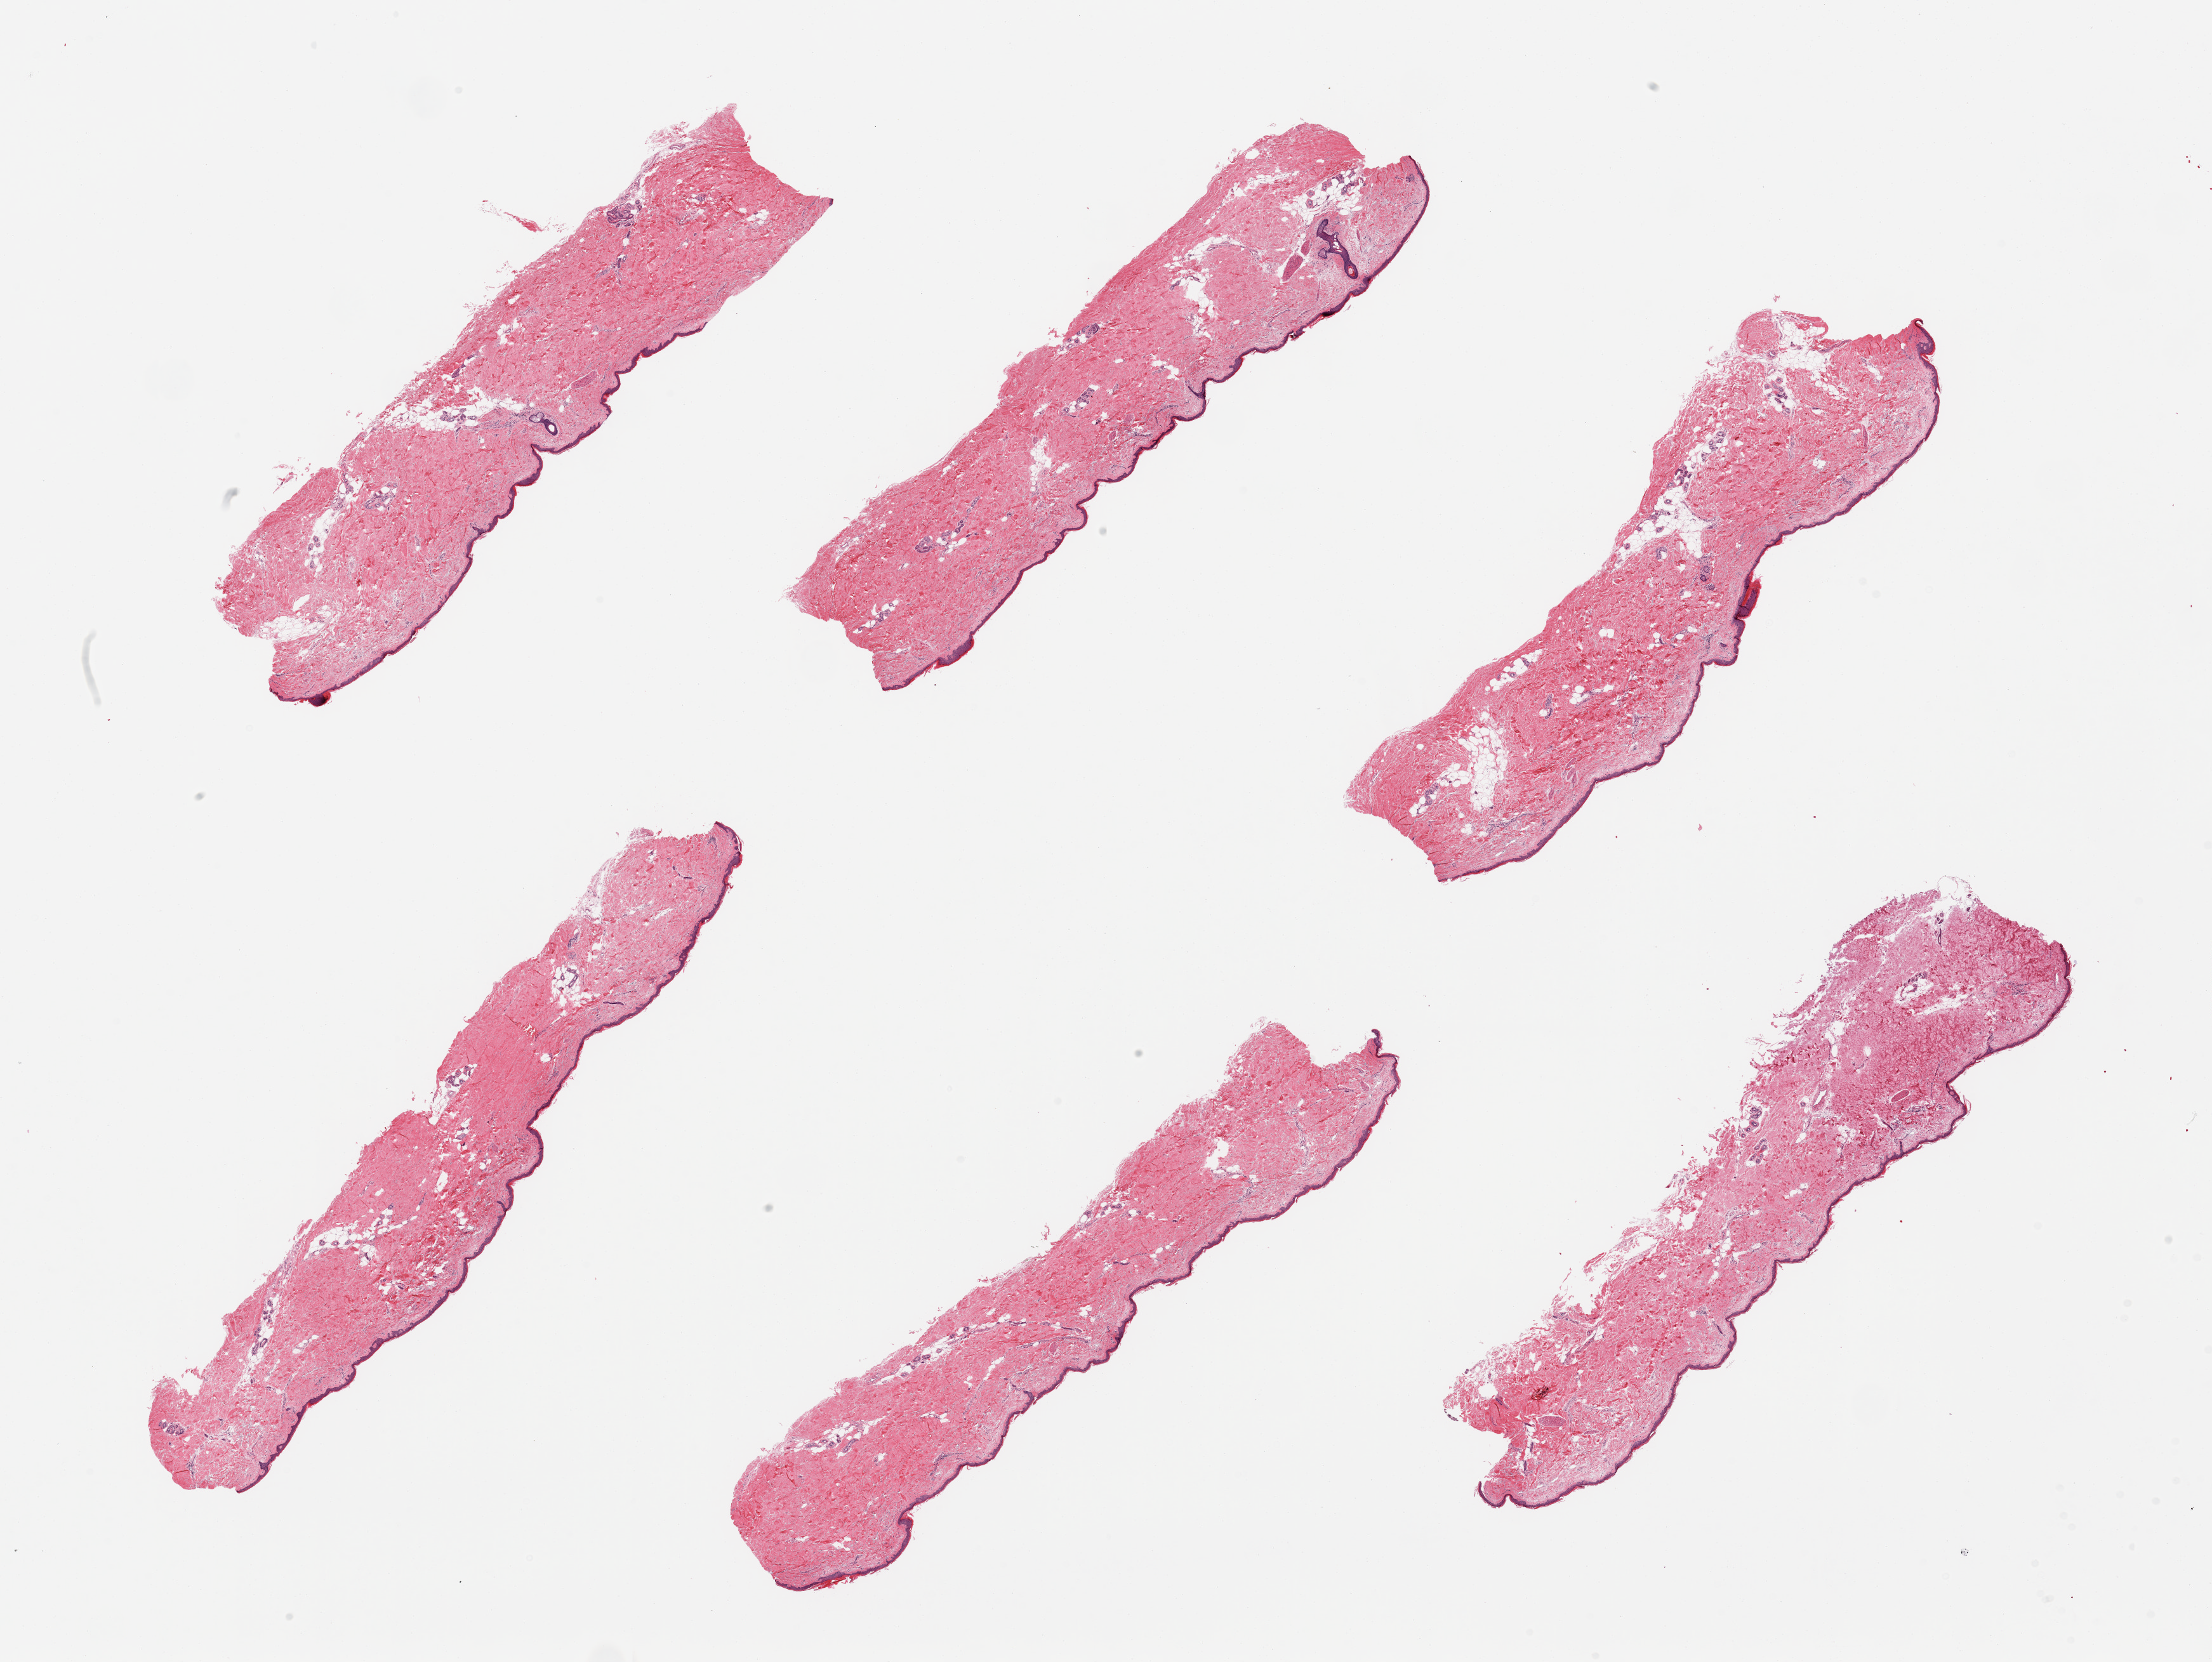
Digitized hematoxylin and eosin (H&E)-stained section — shown as a low-resolution overview of the whole scanned area (about 27.6 x 20.7 mm, slide scanned at 20x); PAXgene-fixed, paraffin-embedded tissue; sampled site (target tissue): skin of lower leg; donor tissue sample. Male donor.
Pathologist's review note for this sample: 6 pieces, squamous epithelium is ~40 microns, no significant dermal fat.